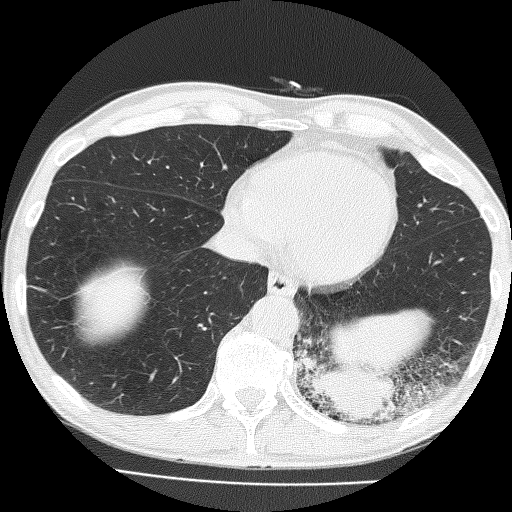
Low-dose screening chest CT, one axial slice. Slice 50 of 160 in the series (ordered by position). 120 kVp. Lung window (W 1500 / L -600 HU). 512 × 512 image matrix, field of view 324 × 324 mm.
Structures marked on this image (expert manual segmentation):
- lesion 1 (tumor, lower lobe of left lung): bounding box <309,365,397,424> (left, top, right, bottom; pixels)